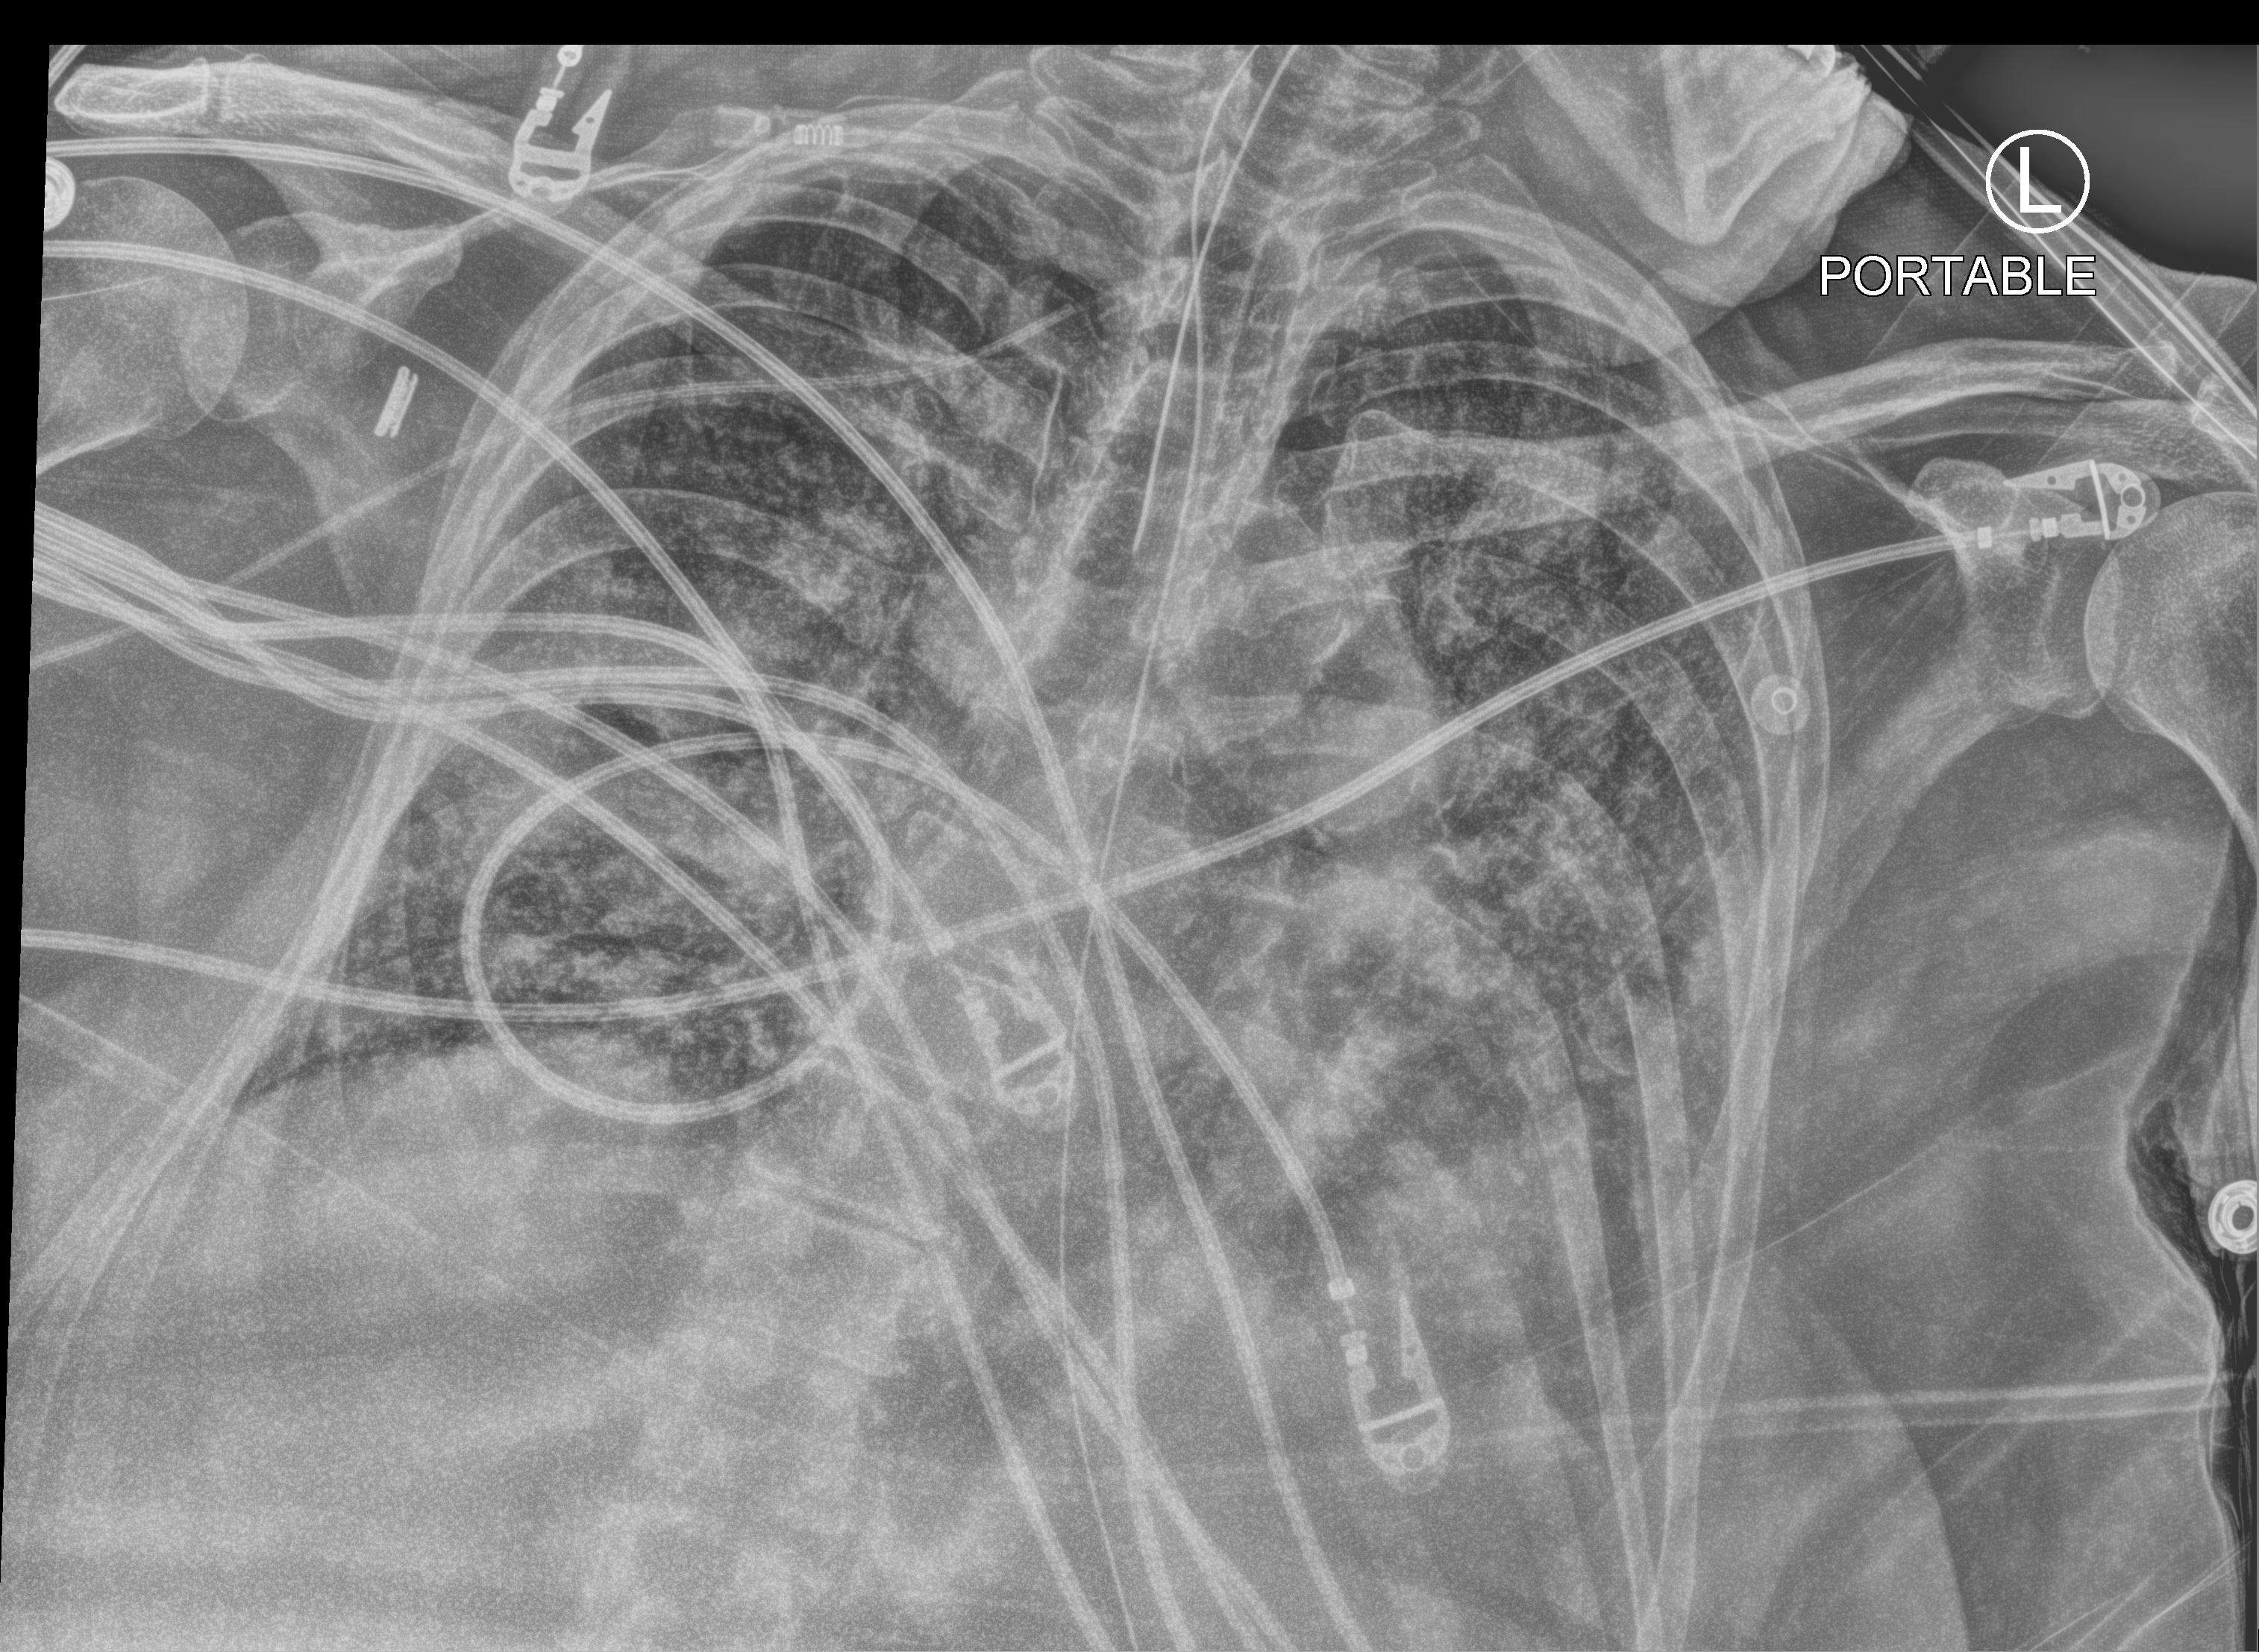
Bedside chest radiograph (computed radiography). Patient hospitalised with COVID-19; female, aged 60–74 years.
Hospital-stay facts (about this admission, not read from this image; timing relative to this image not recorded): diabetes (admission record): no; admitted to intensive care during this hospital stay: yes.